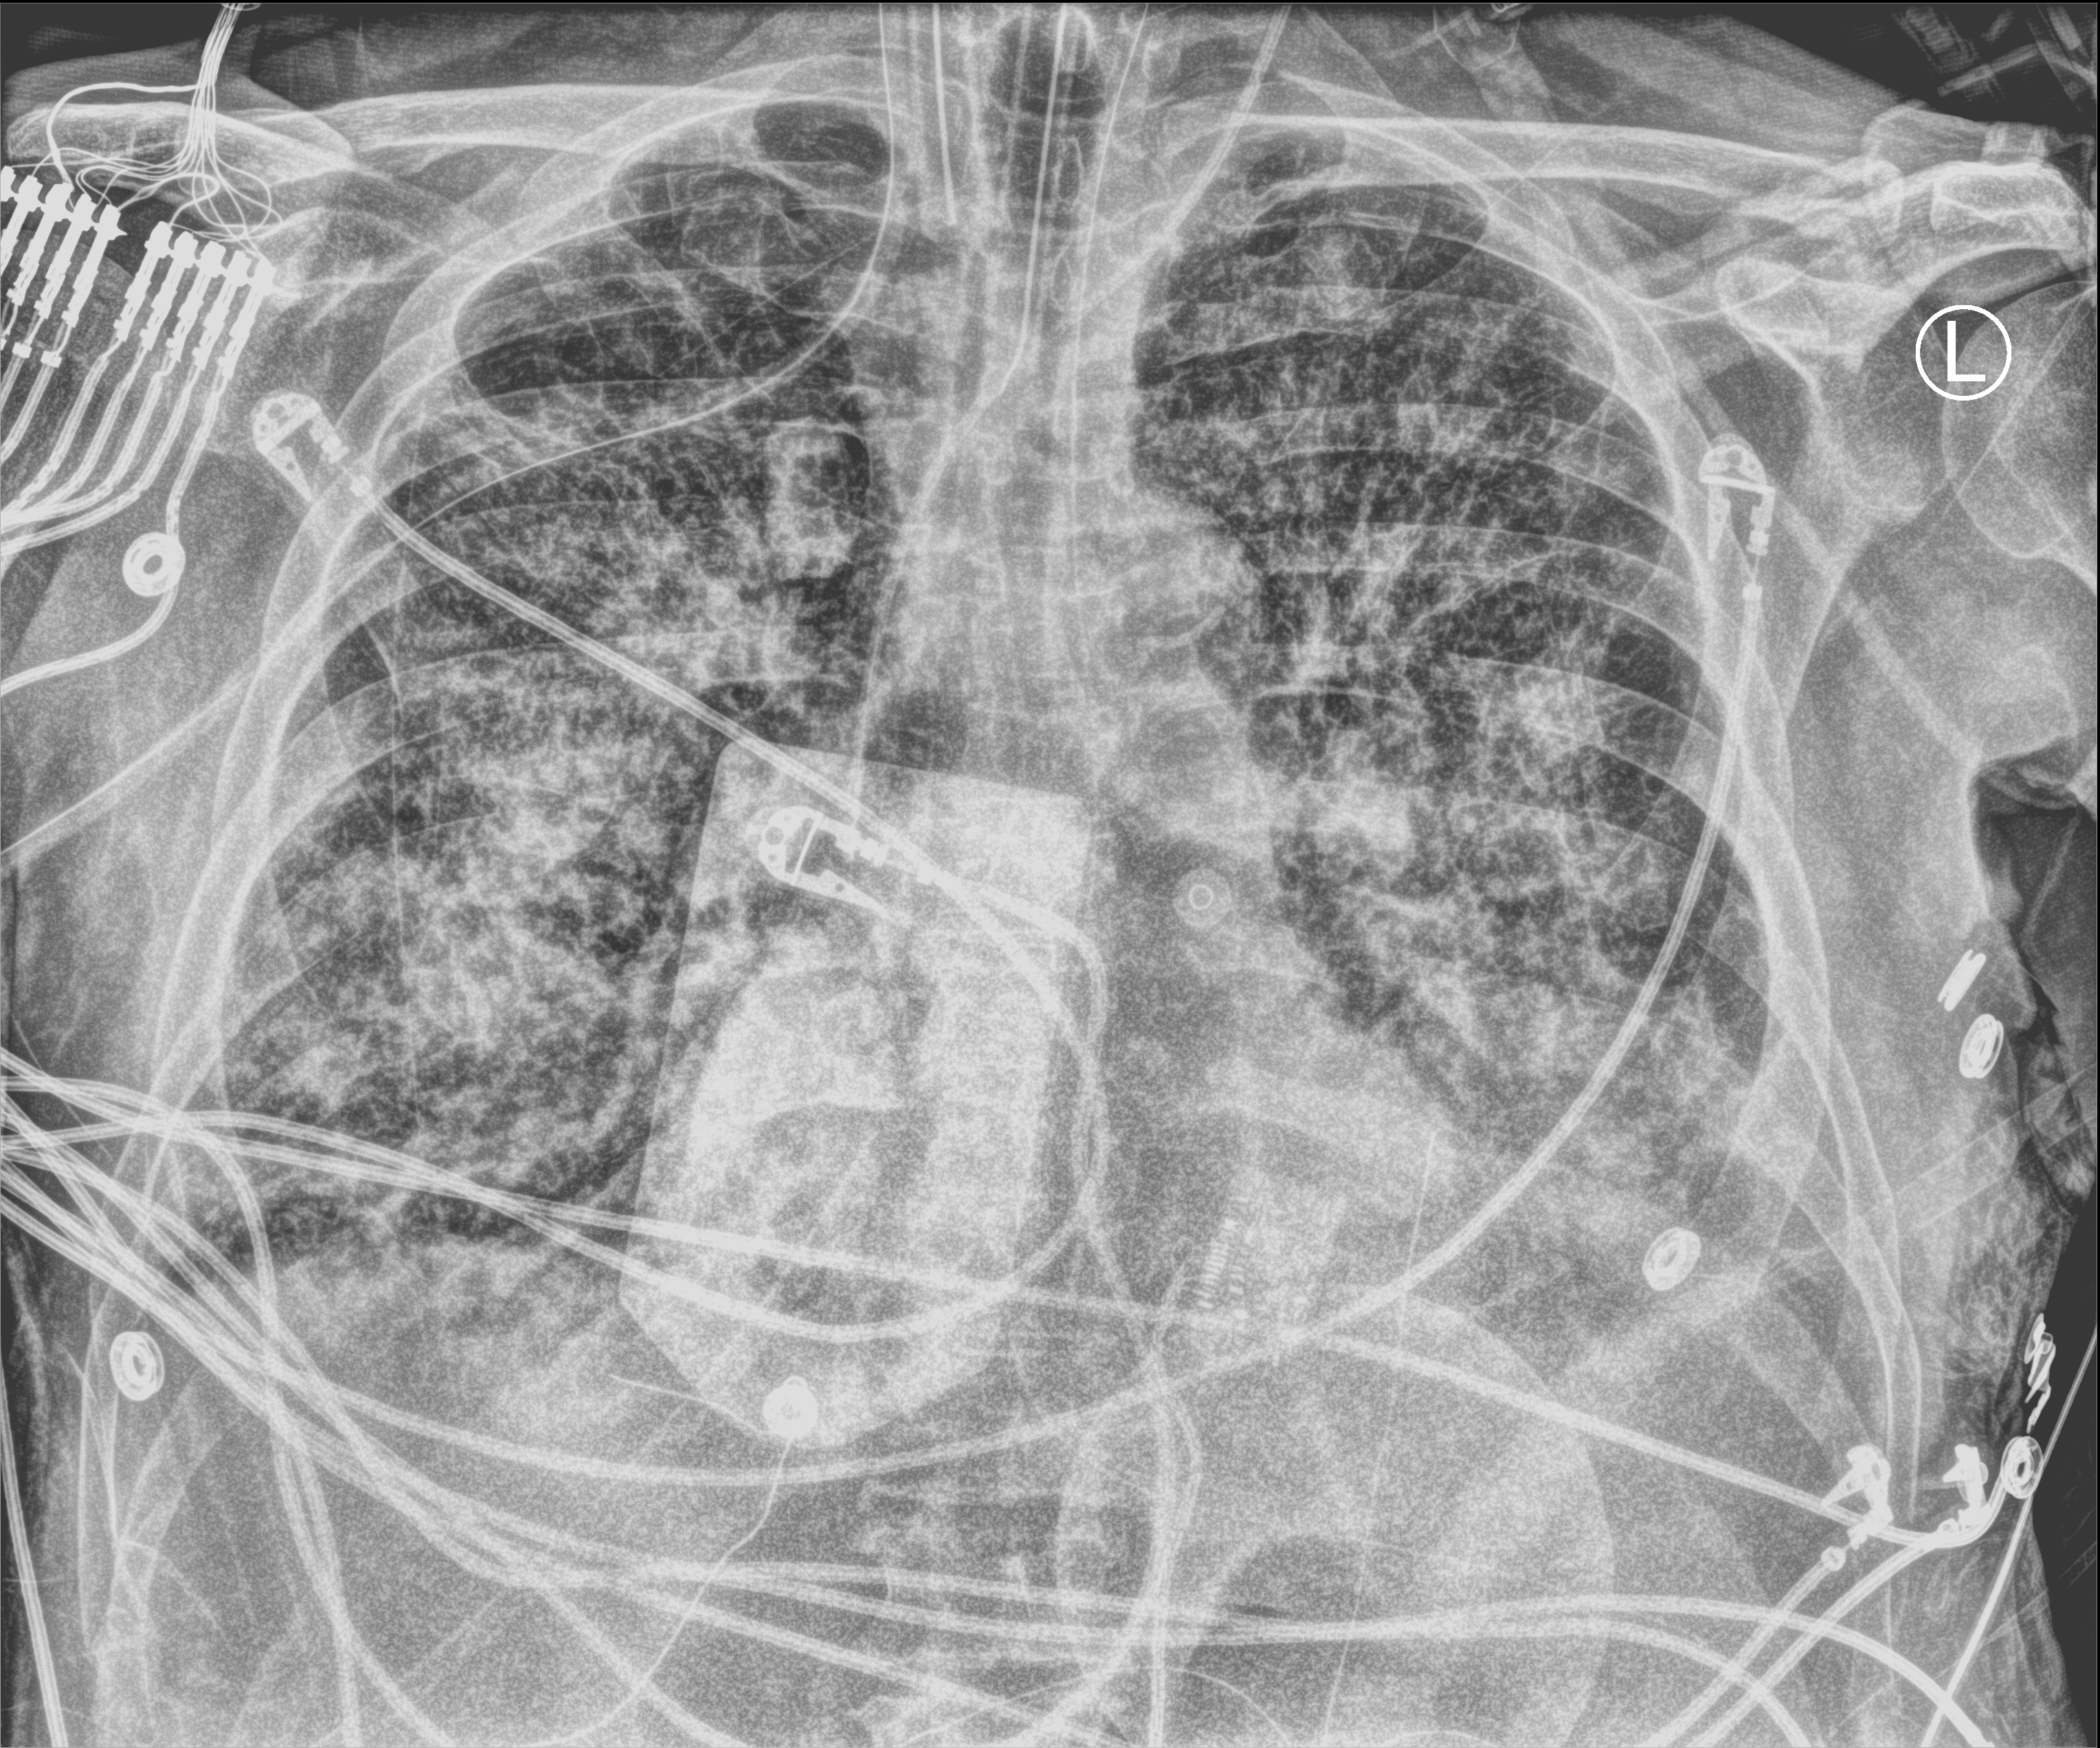
Chest X-ray (portable); anteroposterior (AP) projection. Patient hospitalised with COVID-19; male, aged 75–90 years.
Hospital-stay facts (about this admission, not read from this image; timing relative to this image not recorded):
- chronic kidney disease (admission record): no
- admitted to intensive care during this hospital stay: yes